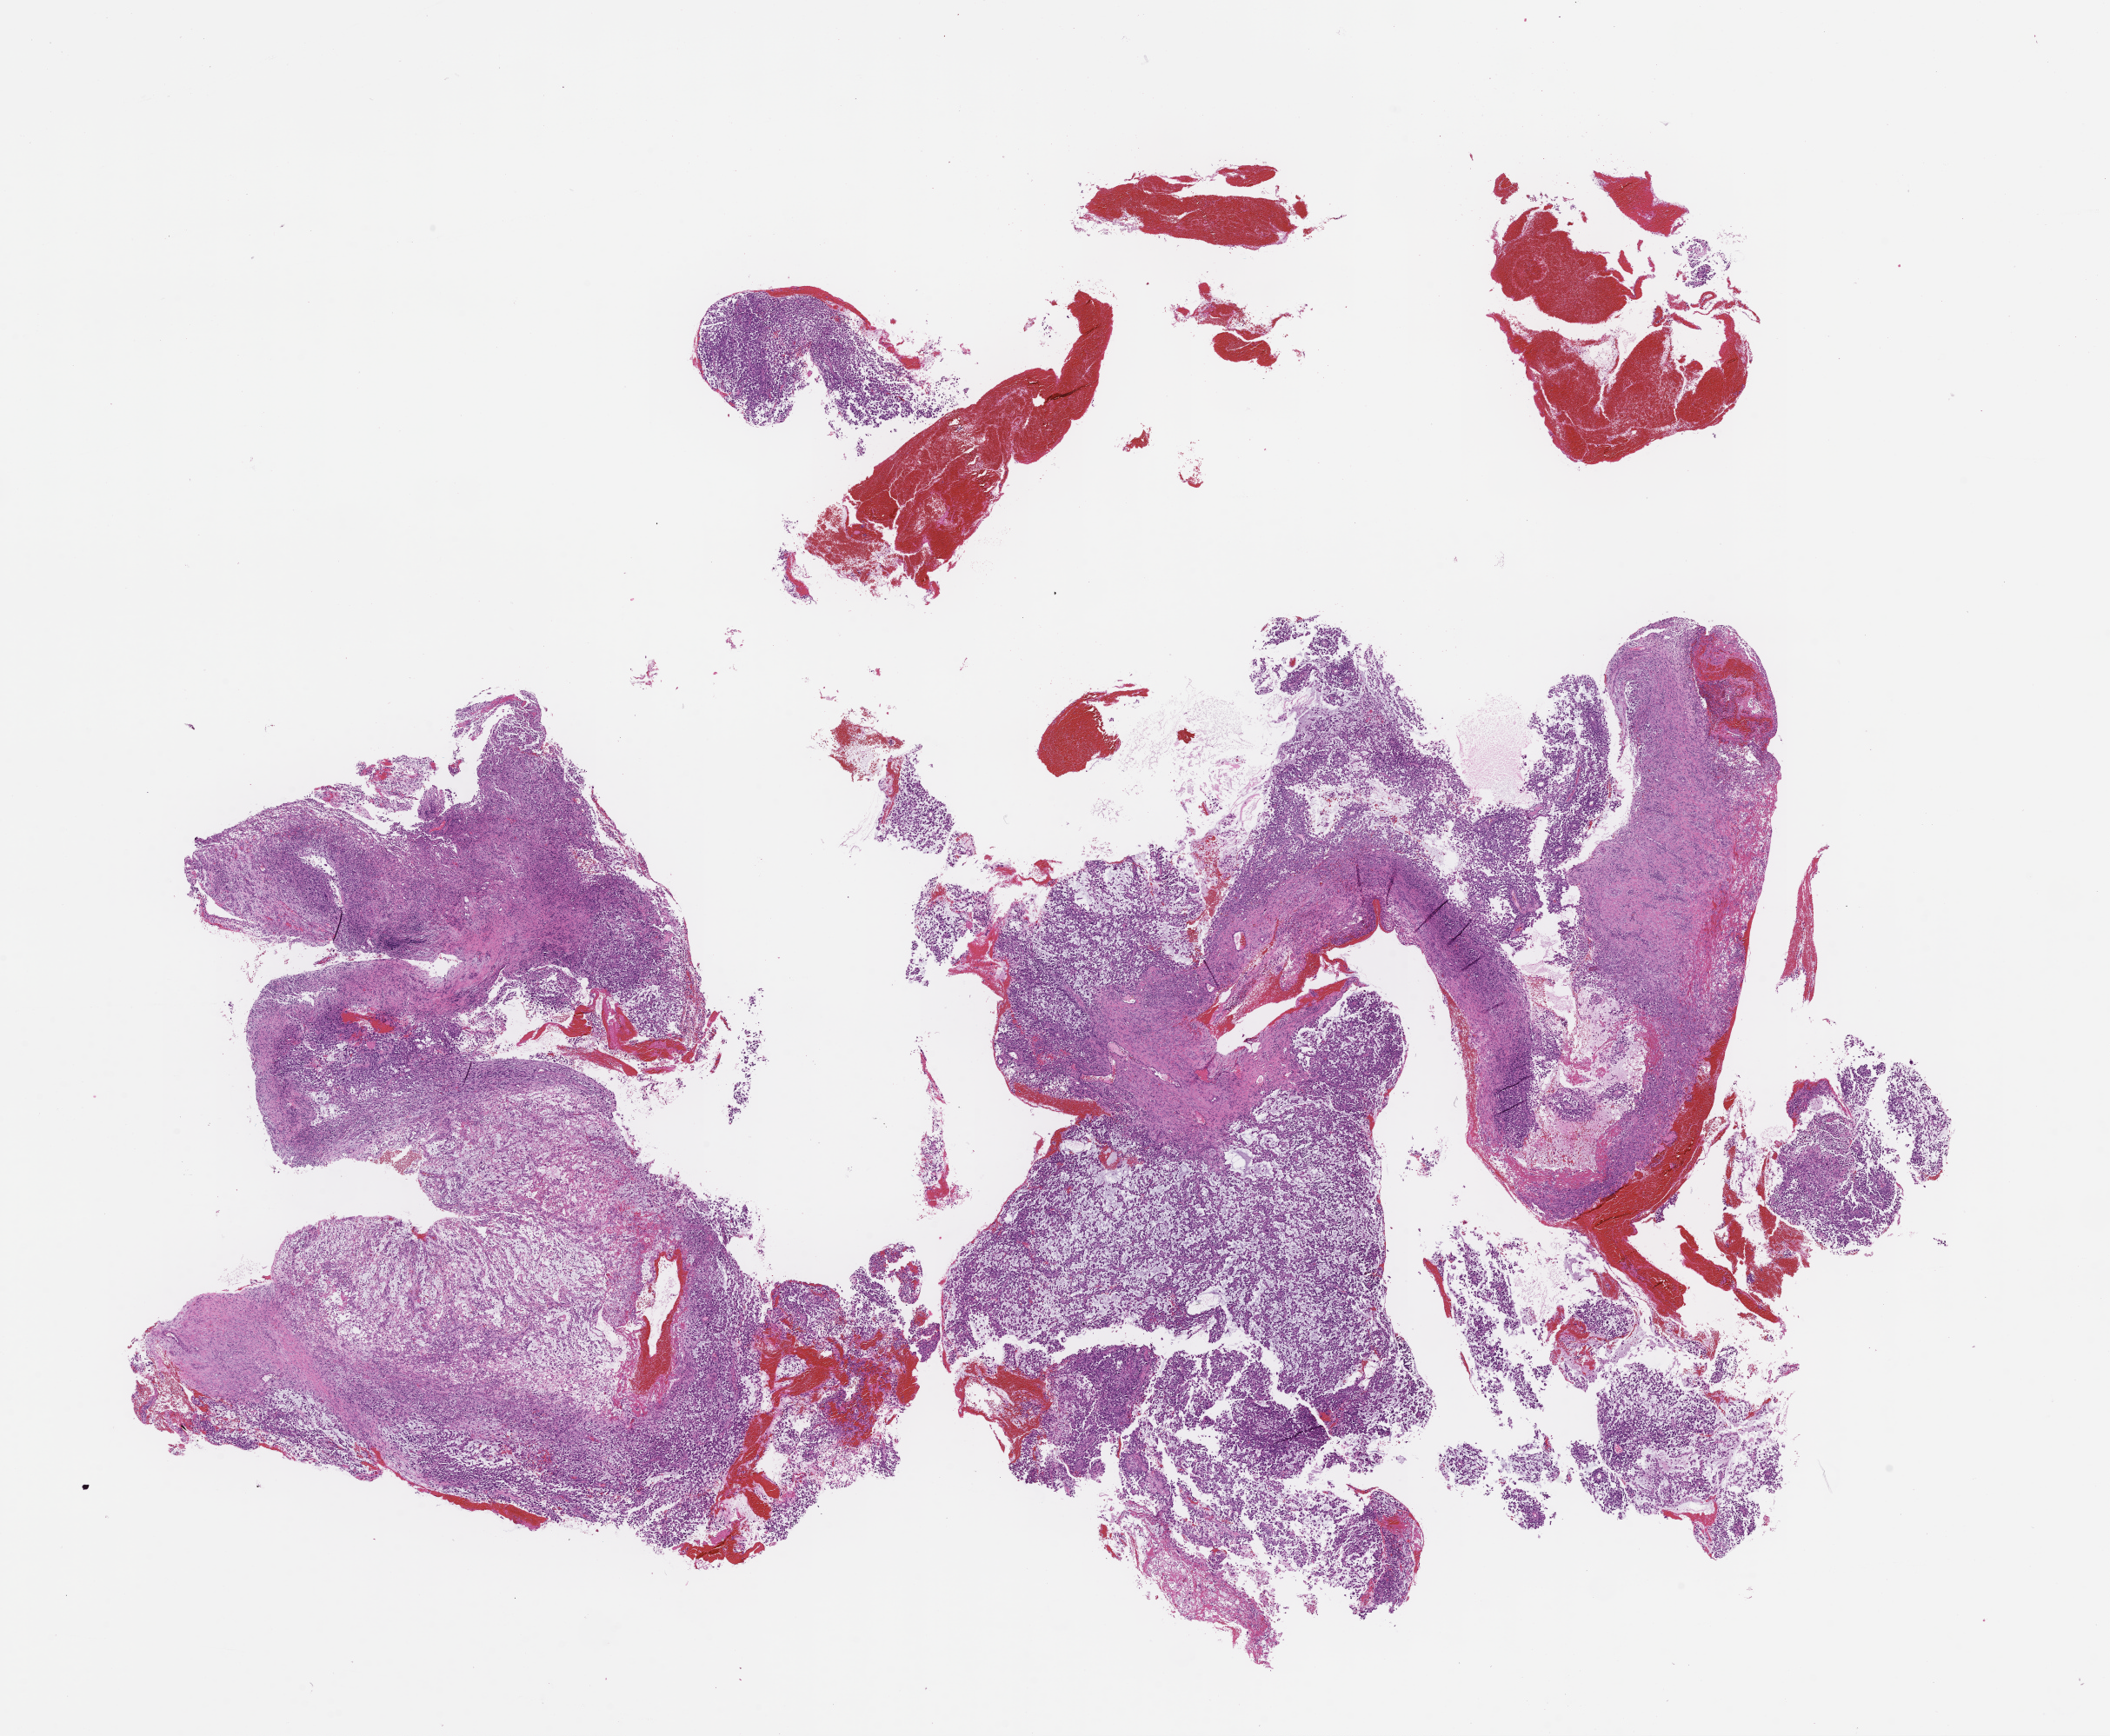
Digitized haematoxylin and eosin-stained section, shown as a low-resolution overview of the whole scanned area (about 19.6 x 16.1 mm); FFPE section; tissue site: lung; specimen time point: archival tissue. Male patient.
- this section: primary tumour tissue
- diagnosis: Non-Small Cell Lung Carcinoma